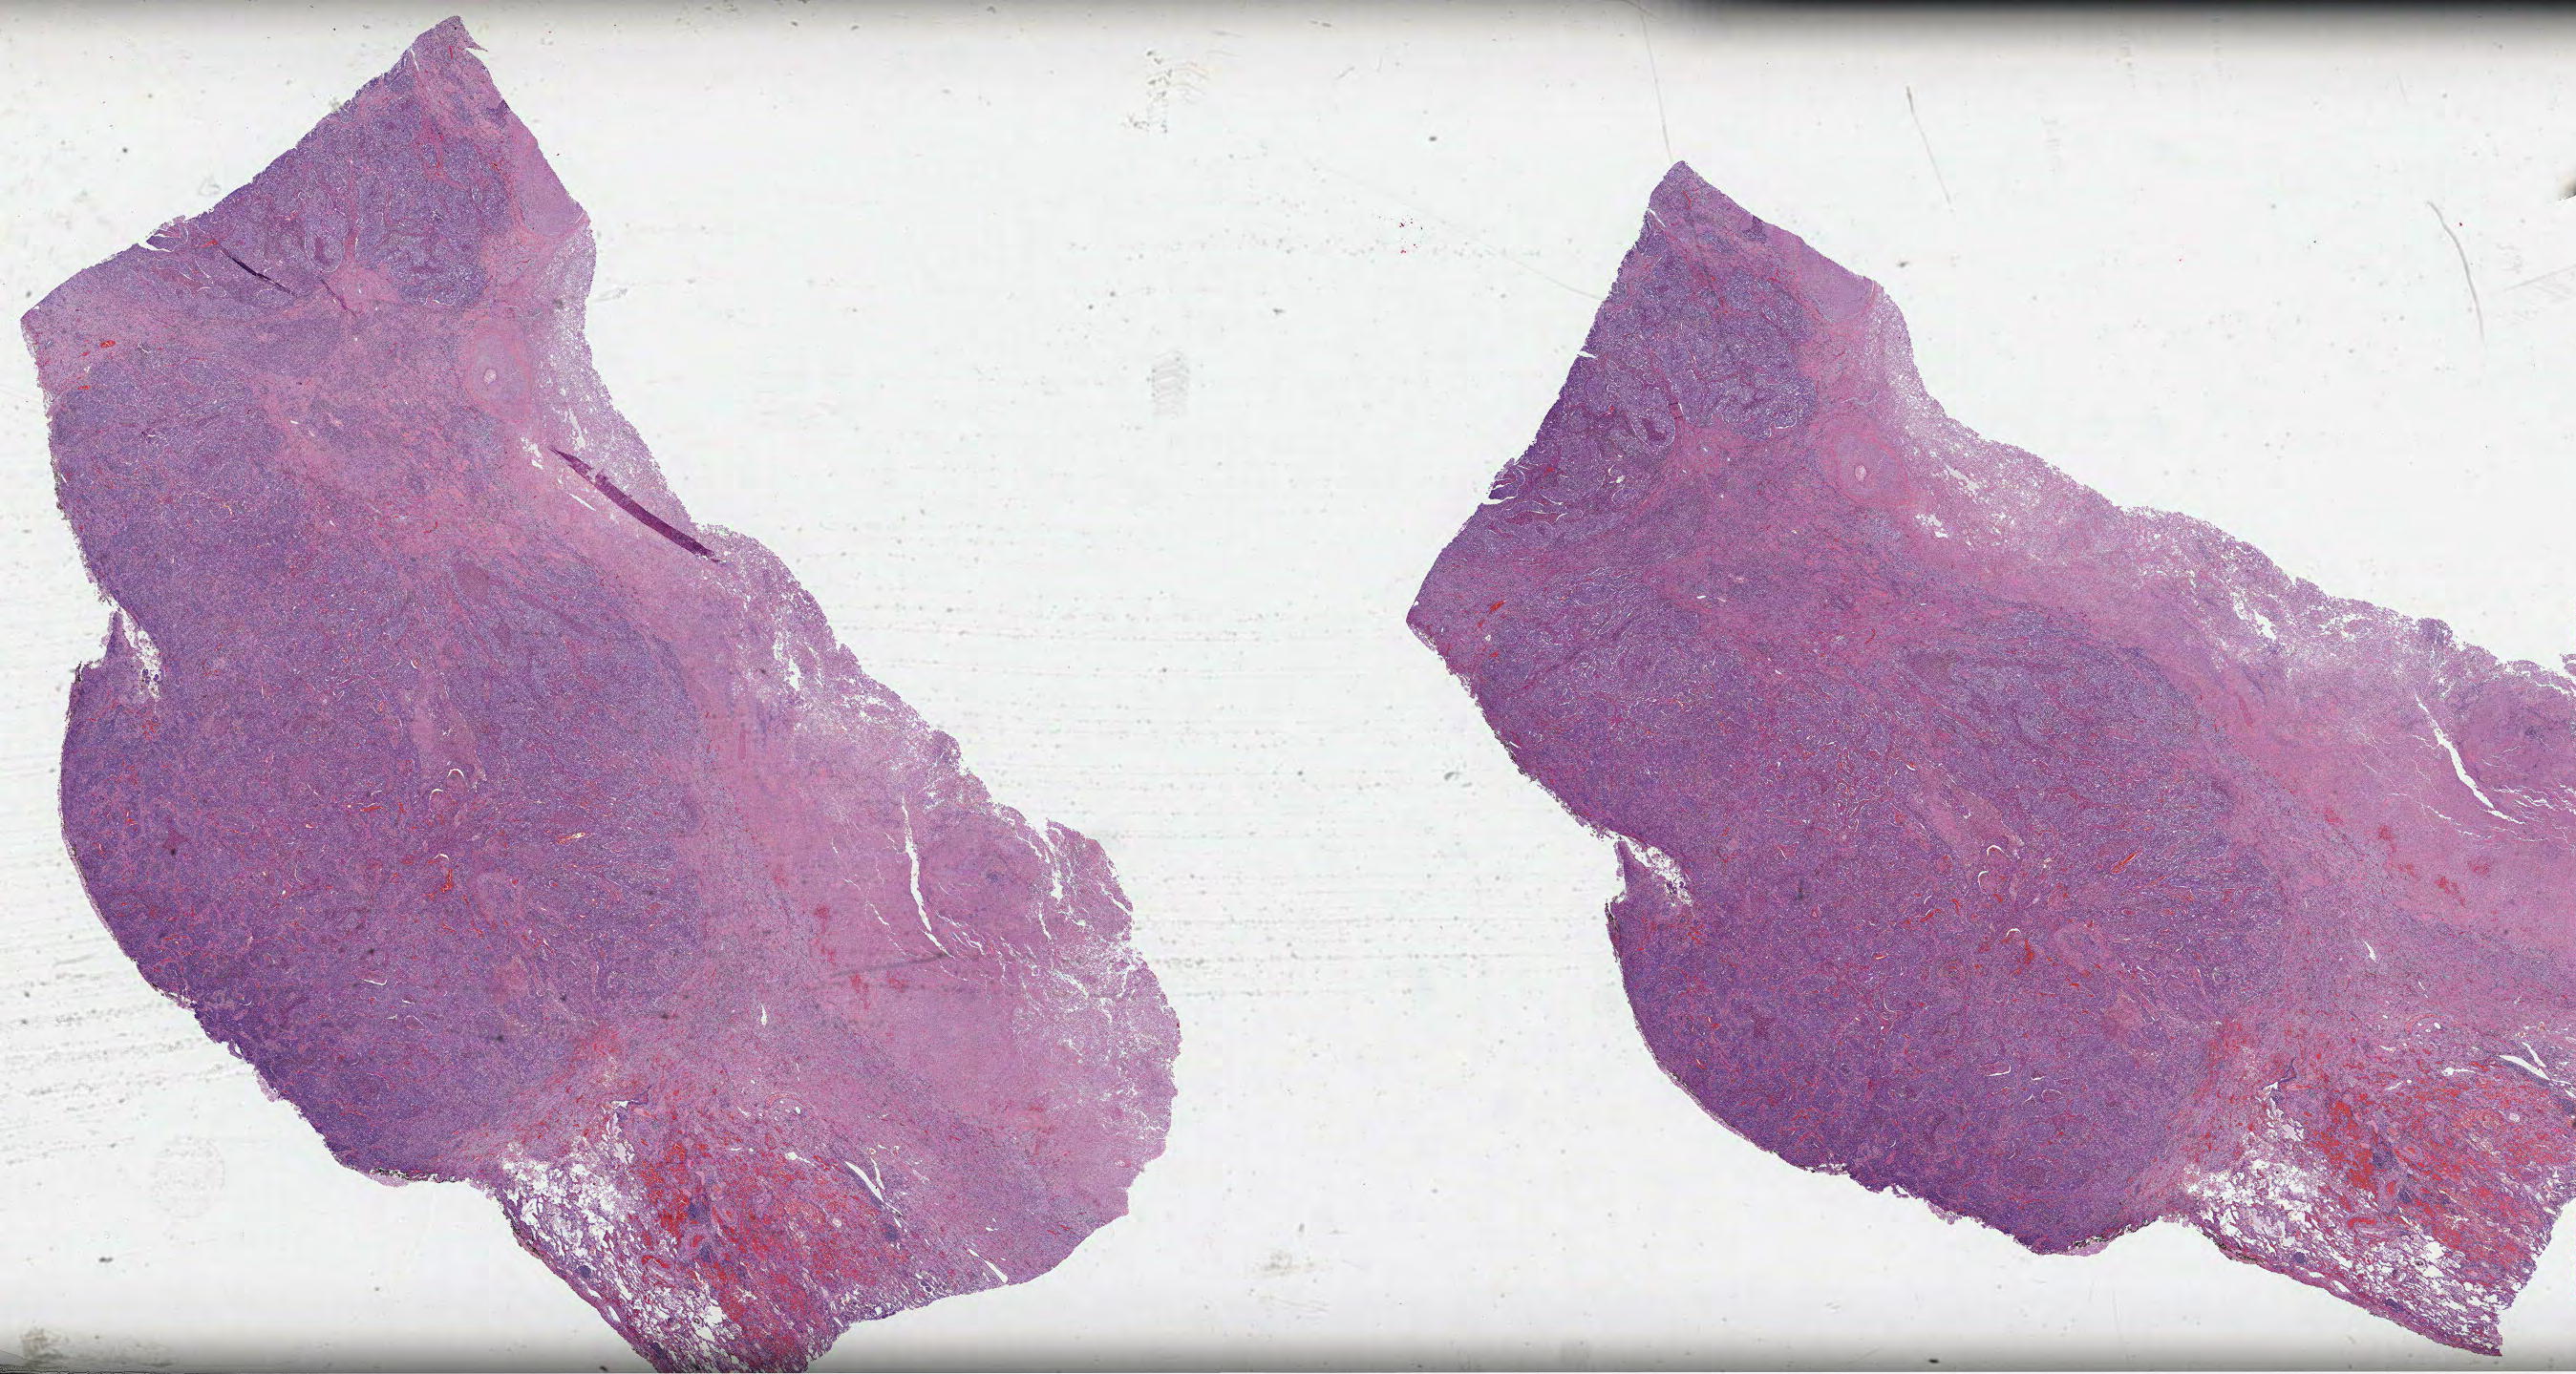
Digitized H&E-stained tissue section (whole slide) — a low-resolution overview of the entire scanned area, about 43.5 x 23.2 mm; formalin-fixed paraffin-embedded (FFPE) diagnostic section; sample: primary tumour, lung. Male, age 68 years at initial diagnosis.
Diagnosis: Squamous cell carcinoma, NOS.